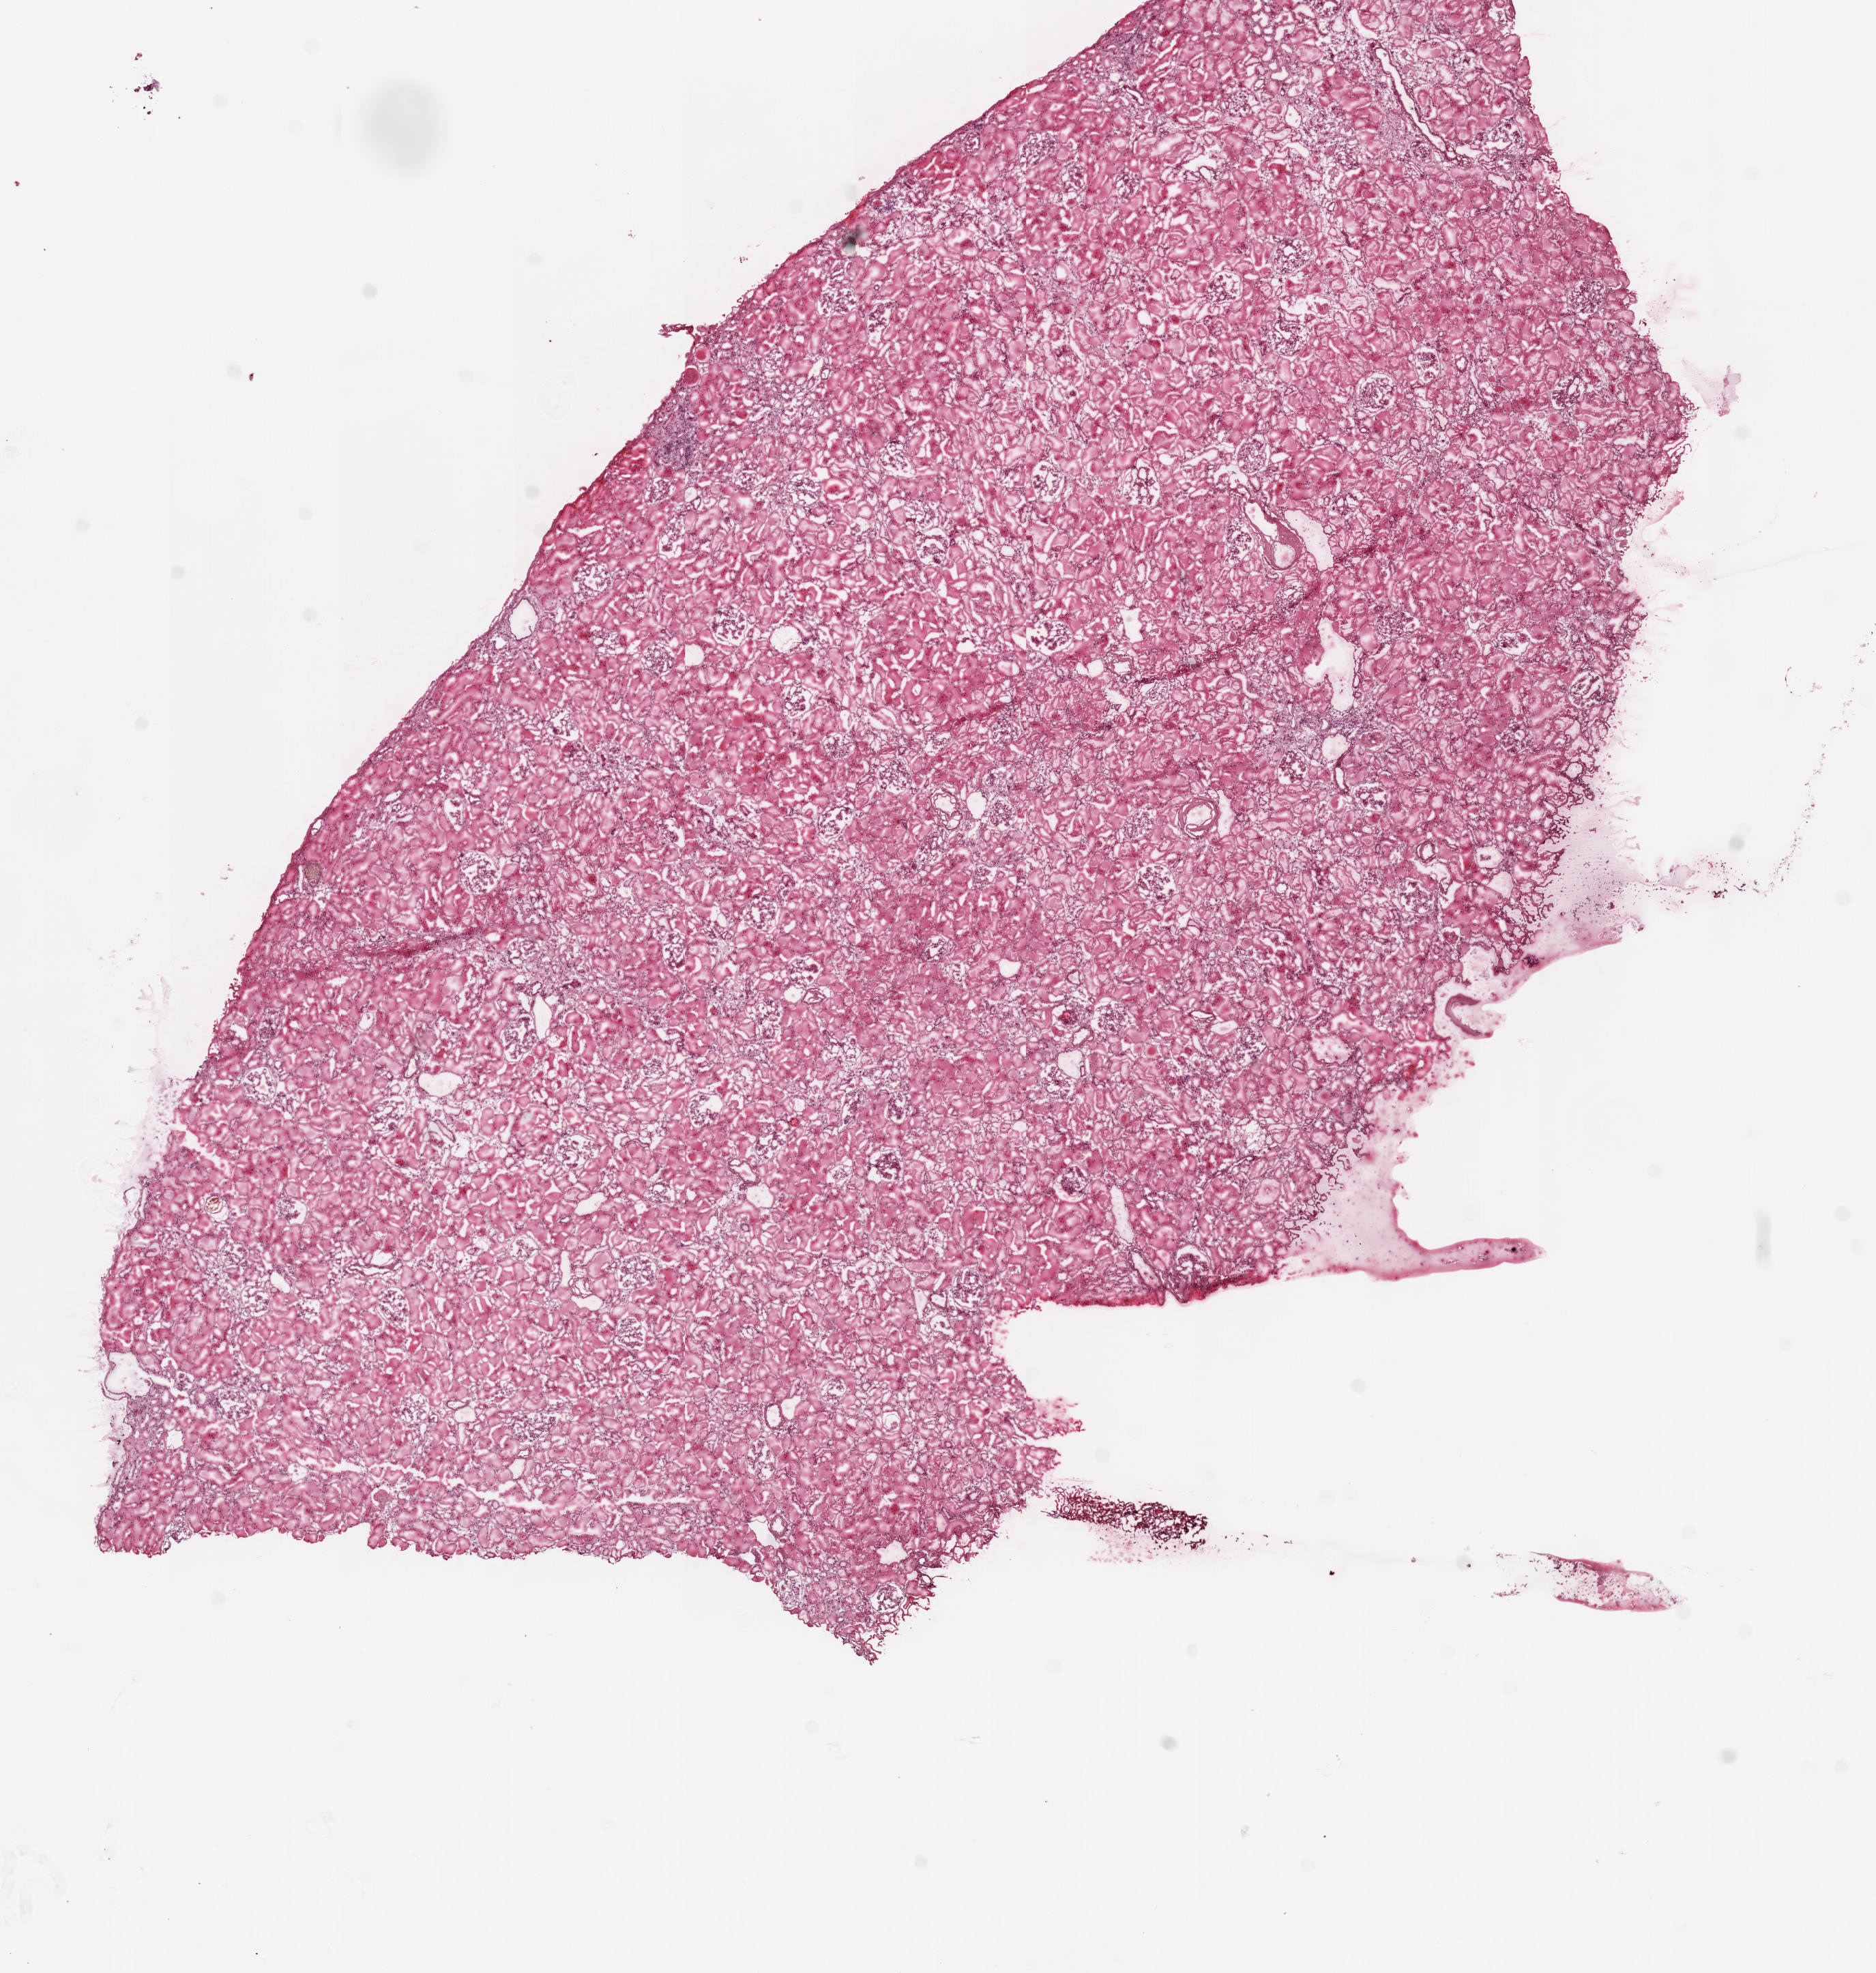
H&E whole-slide image, a low-resolution overview of the entire scanned area, about 11.0 x 11.6 mm (from a 20x scan). Frozen section from the top of the tissue portion. Solid tissue normal (non-tumour tissue) sample from the kidney. Patient: female, age at initial diagnosis 78 years.
- this section: solid tissue normal sample (biorepository sample class)
- patient diagnosis: Clear cell adenocarcinoma, NOS